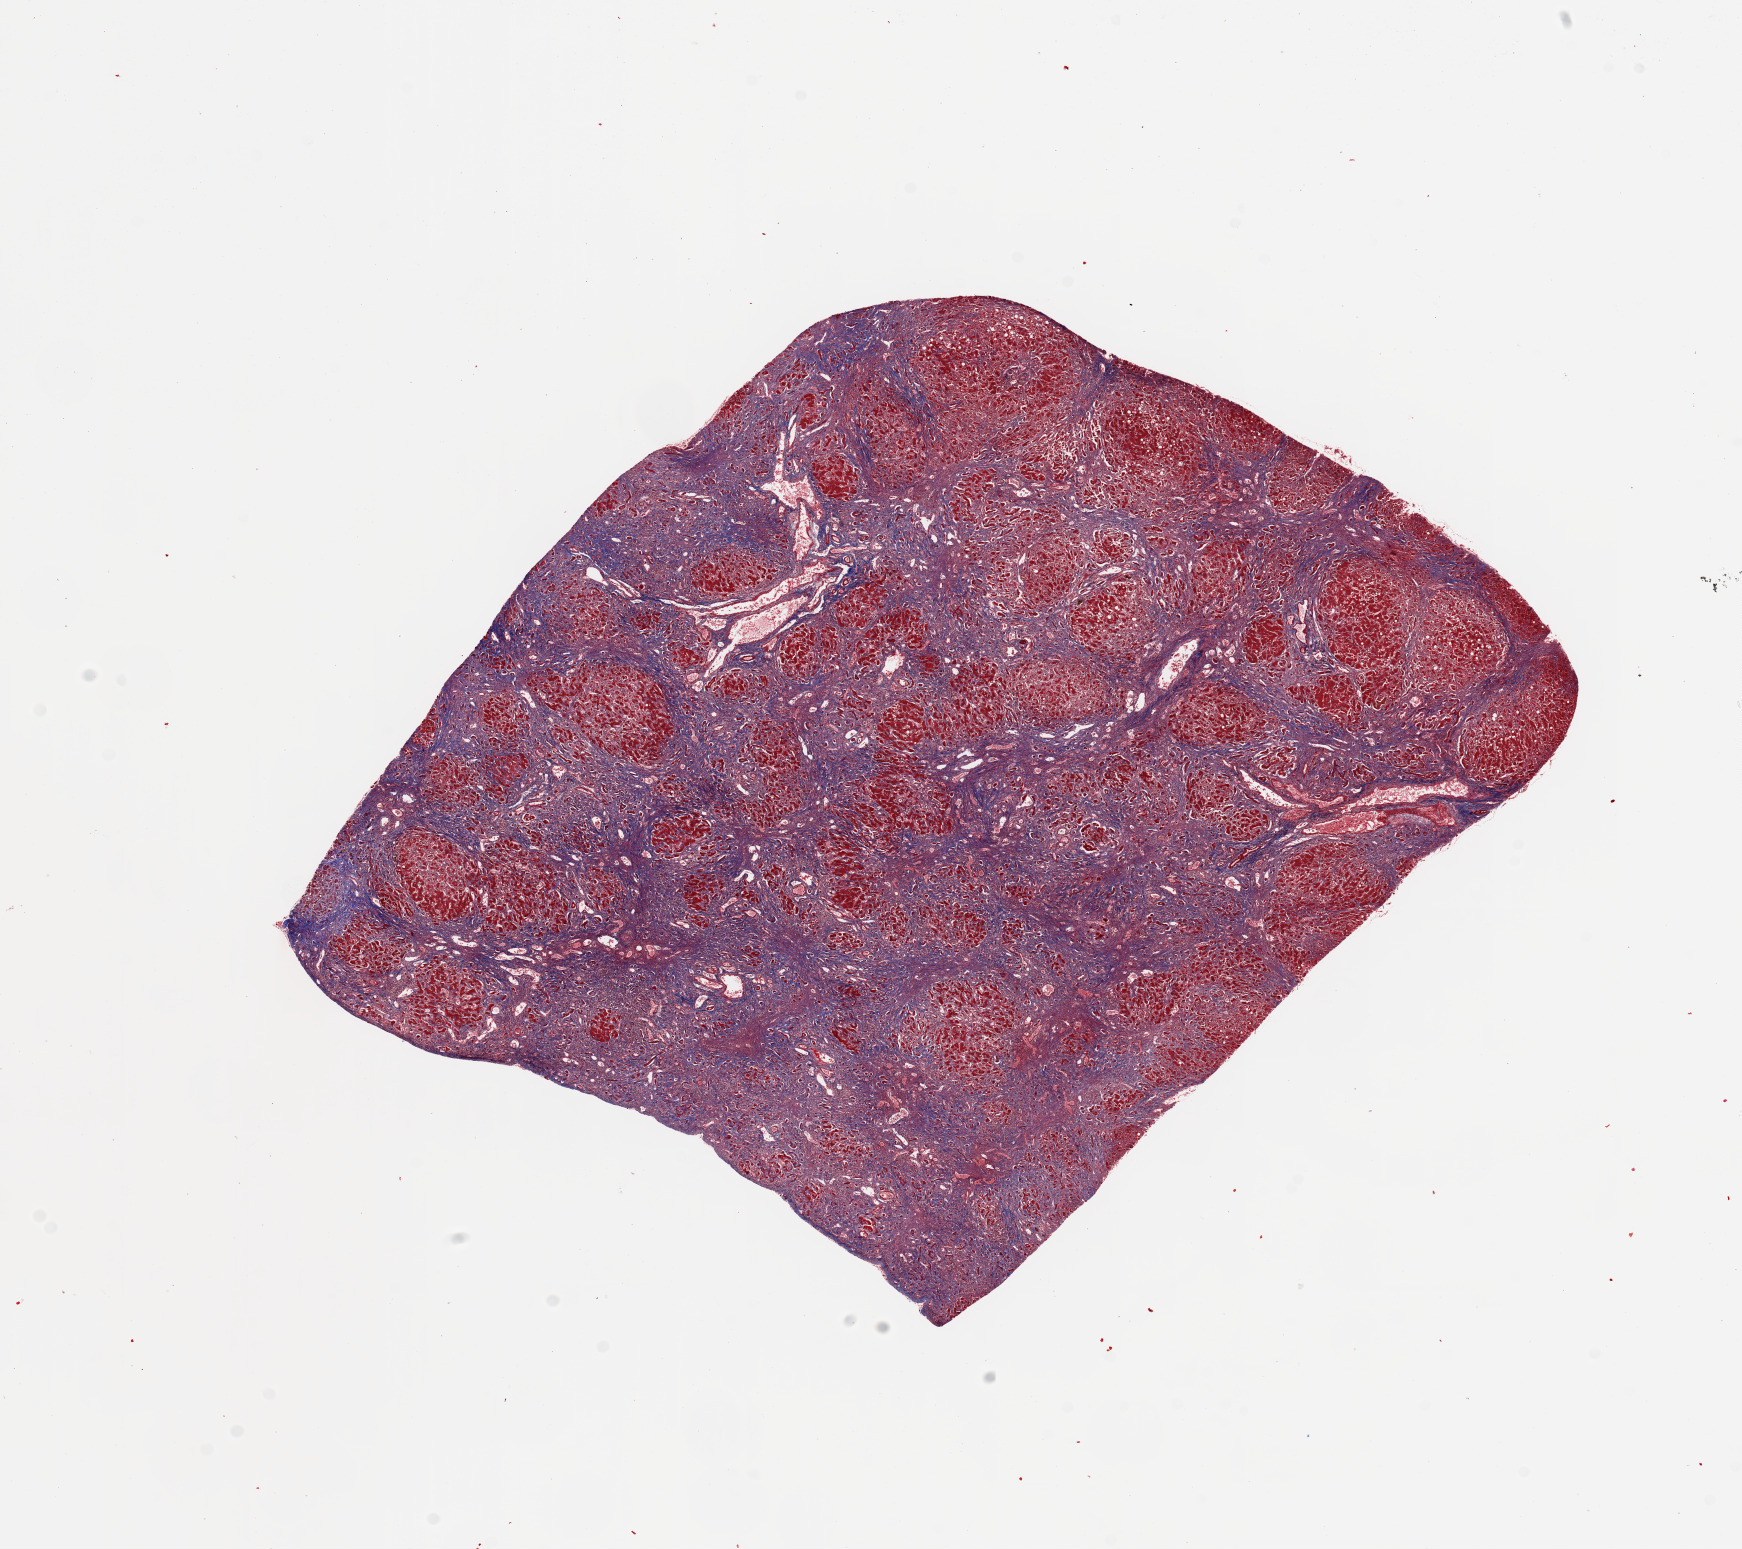
Whole-slide image, H&E stain, shown as a low-resolution overview of the whole scanned area (about 13.8 x 12.3 mm, acquisition: 20x scan). PAXgene-fixed, paraffin-embedded tissue. Section of liver (target tissue). Tissue donor sample. Donor: male.
- reviewer comment on this tissue sample: ~10x8mm. Appears cirrhotic, request trichrome